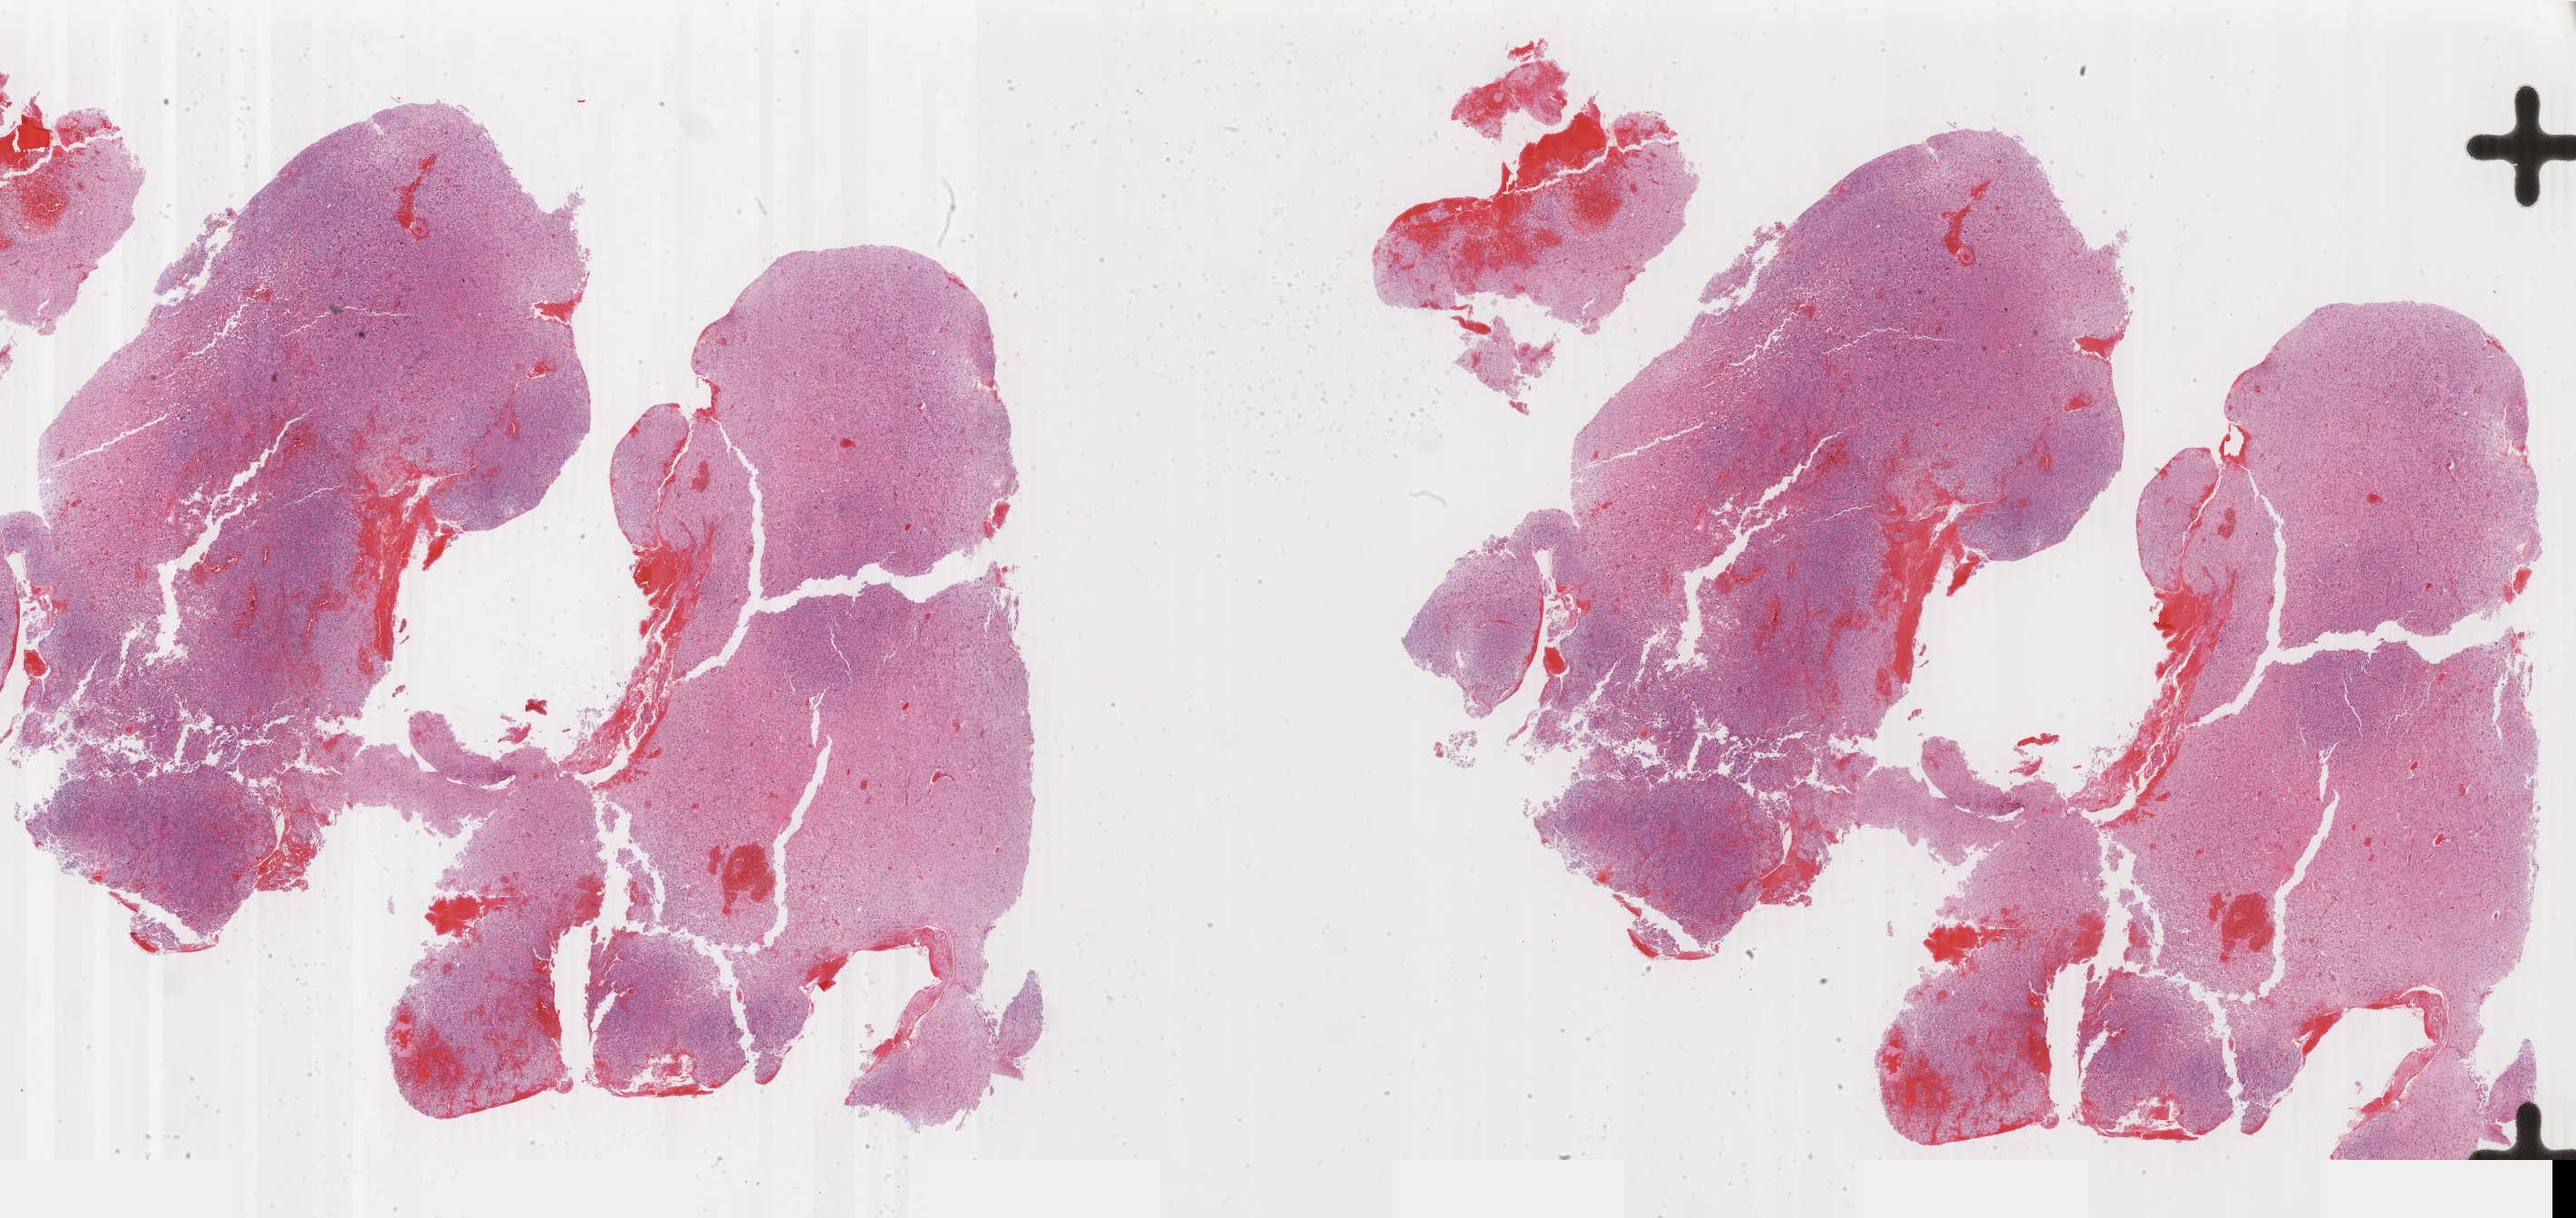
Digitized Hematoxylin and eosin (H&E) stained tissue section (whole slide), whole scanned area (about 45.2 x 21.4 mm) shown as a low-resolution overview; FFPE section; brain, primary tumour sample. Male patient; age at initial diagnosis 59 years.
Histologic diagnosis: Glioblastoma.